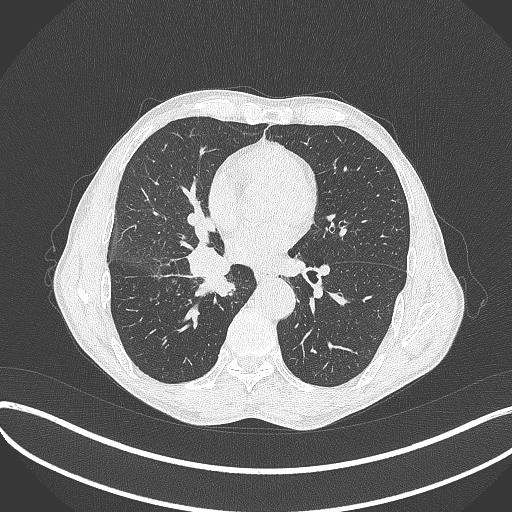
Chest CT, one axial slice; slice 203 of 481 in the series (ordered by position); 120 kVp; lung window (W 1500 / L -600 HU); 1 mm slice thickness; 512 × 512 image matrix. Male patient, age 65 years. Case-level facts recorded for this patient, not image findings: clinical TNM (as recorded): T2a N0 M0; histopathological grade: G2.
Annotated regions visible in this slice (bounding box drawn by a radiologist):
- lung tumour (recorded histology: squamous cell carcinoma): bounding box [x1, y1, x2, y2] px = [181, 239, 237, 298]